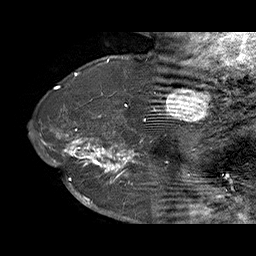
Breast MRI (dynamic contrast-enhanced), one sagittal slice; position 51 of 70 along the scan axis; dynamic contrast-enhanced series, time point 2 of 6 at this slice position (early post-contrast); 1.5 T; TE 4.5 ms, TR 32.4 ms; 256 × 256 image matrix, field of view 180 × 180 mm. Female patient. From the clinical record (not read from this slice): setting: breast cancer imaged before/during neoadjuvant chemotherapy; receptor status: HR-positive, HER2-negative.
Outlined on this slice (semi-automatic segmentation, software-assisted and operator-edited):
- analysis volume of interest (the breast-tissue region the enhancement analysis was run in; not a lesion): box from (x=71, y=128) to (x=159, y=202) px
- tumour enhancement mask (voxels above the 100 % enhancement threshold inside the analysis volume of interest): (x=71, y=129)–(x=142, y=202)